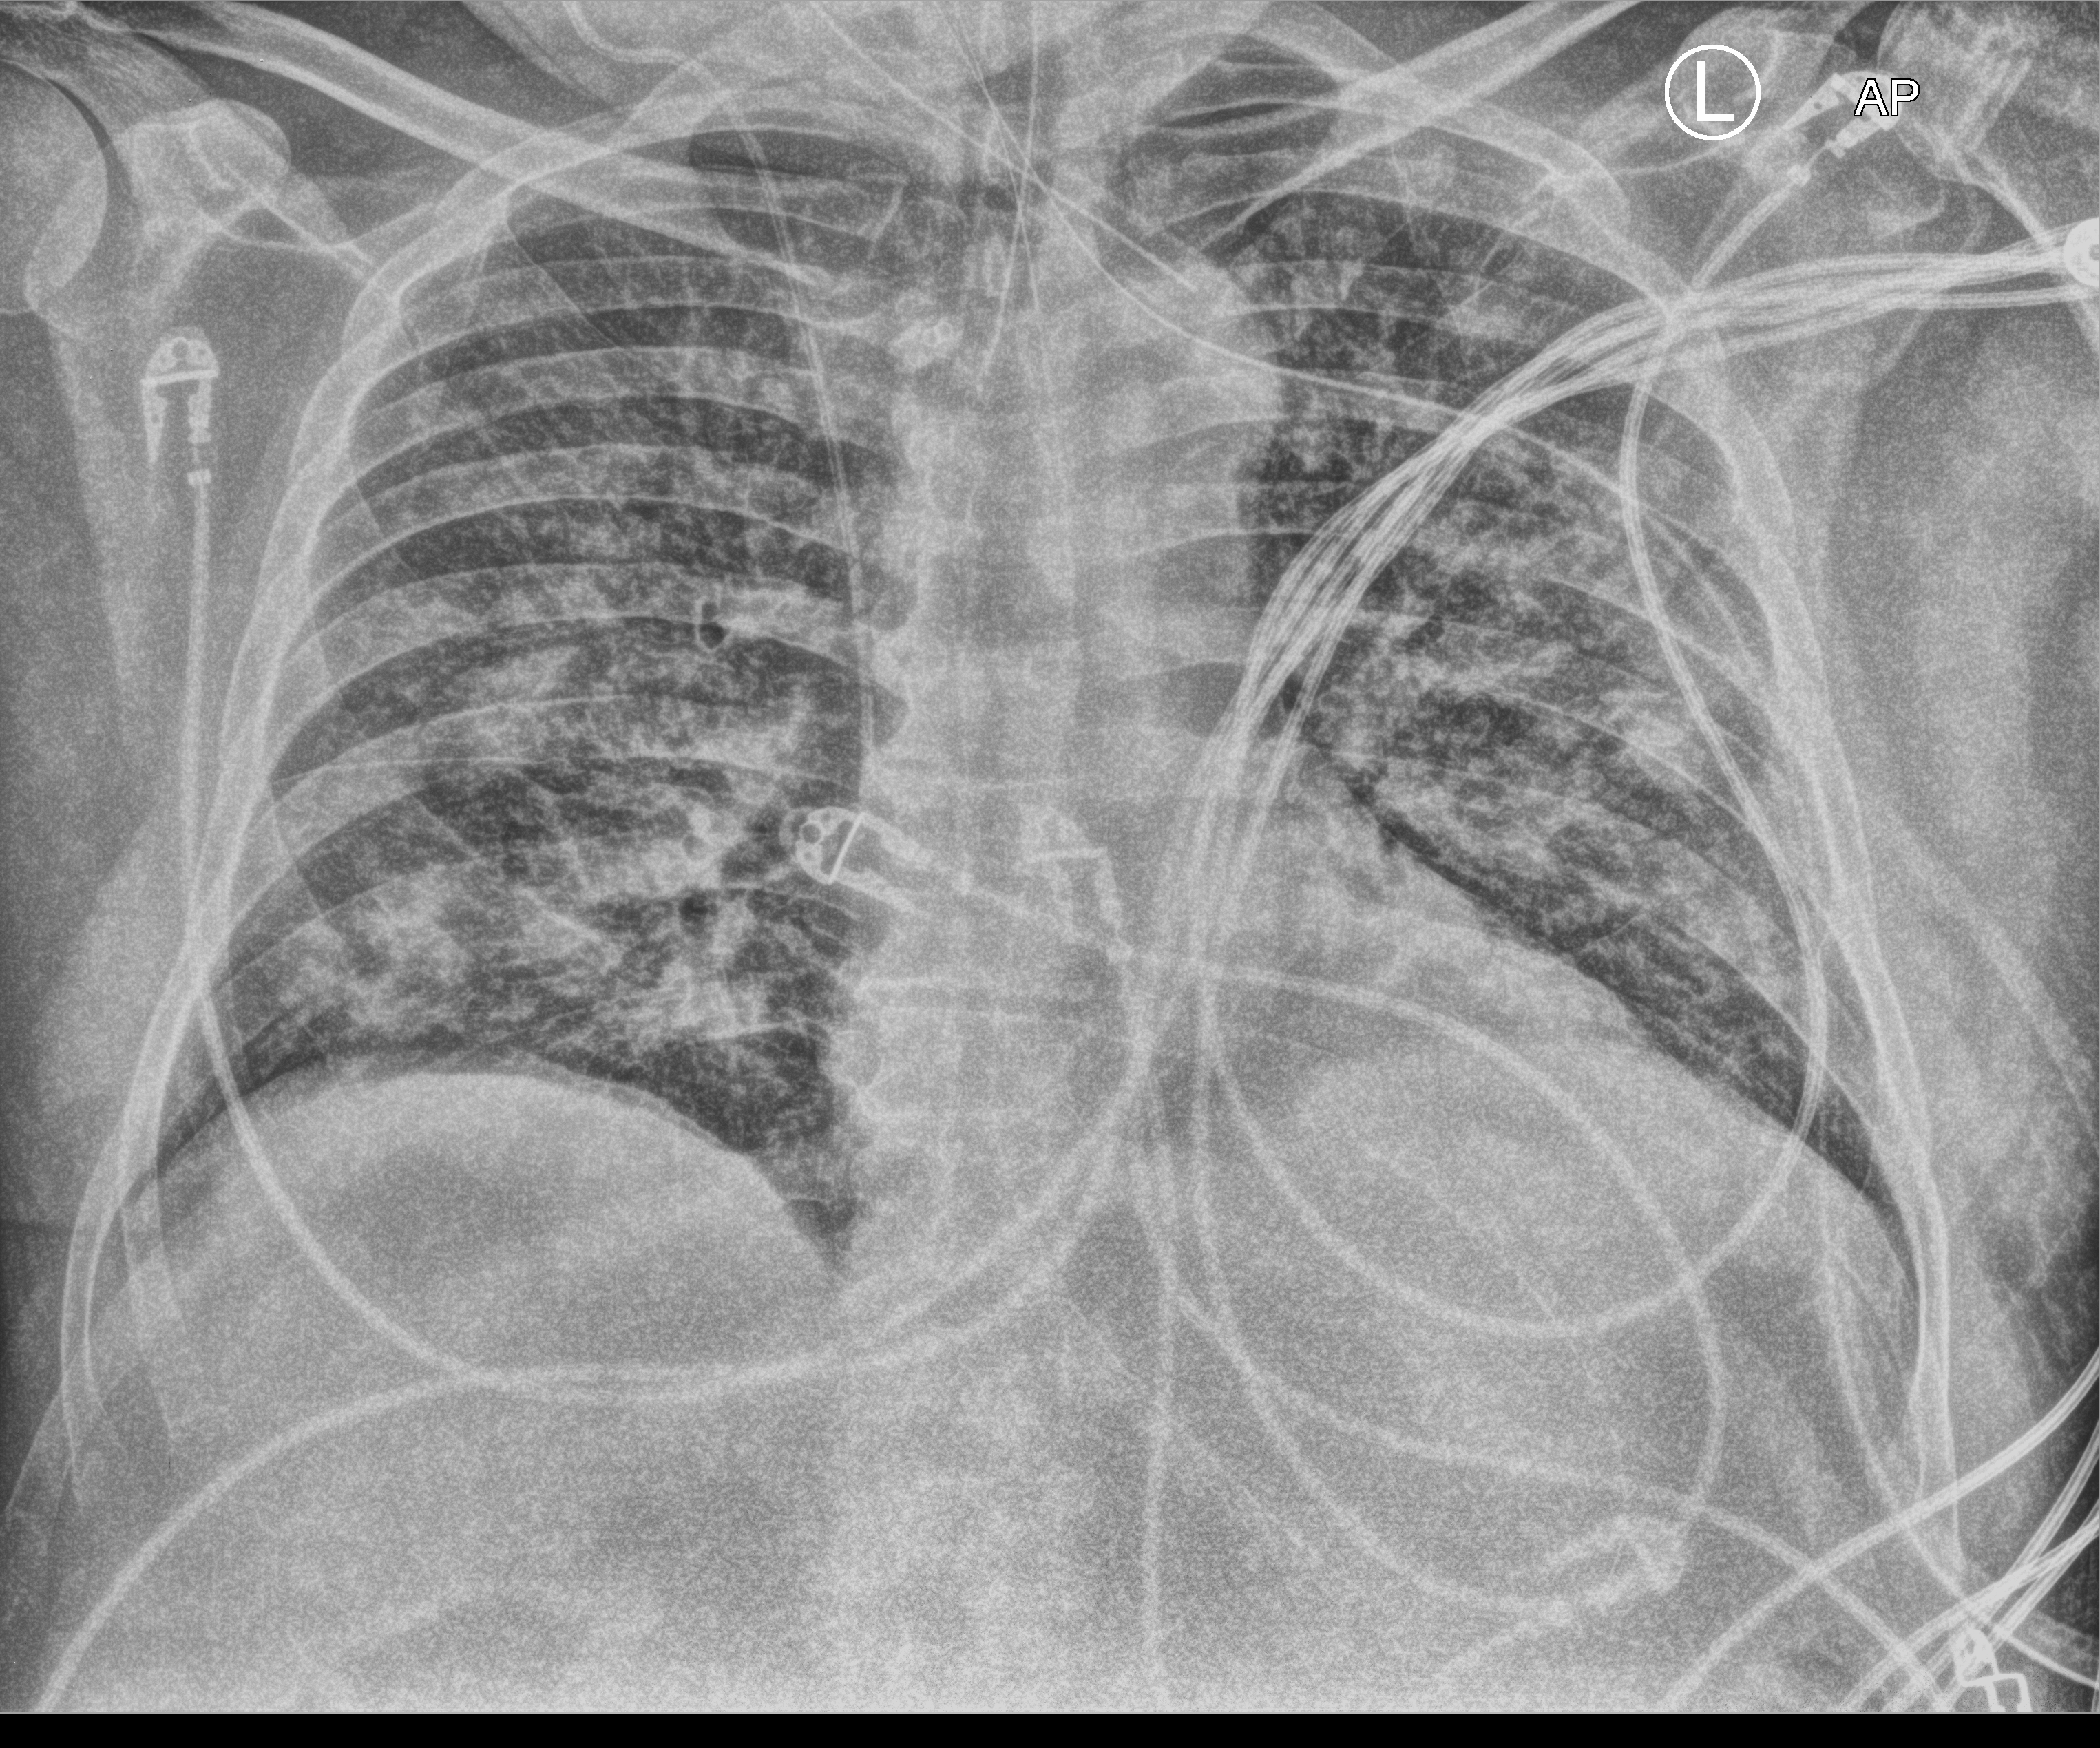
Chest X-ray (portable); anteroposterior (AP) projection. Male patient hospitalised with COVID-19, age 60–74 years.
Hospital-stay facts (about this admission, not read from this image; timing relative to this image not recorded): chronic kidney disease (admission record): no; mechanically ventilated during this hospital stay: yes; admitted to intensive care during this hospital stay: yes.